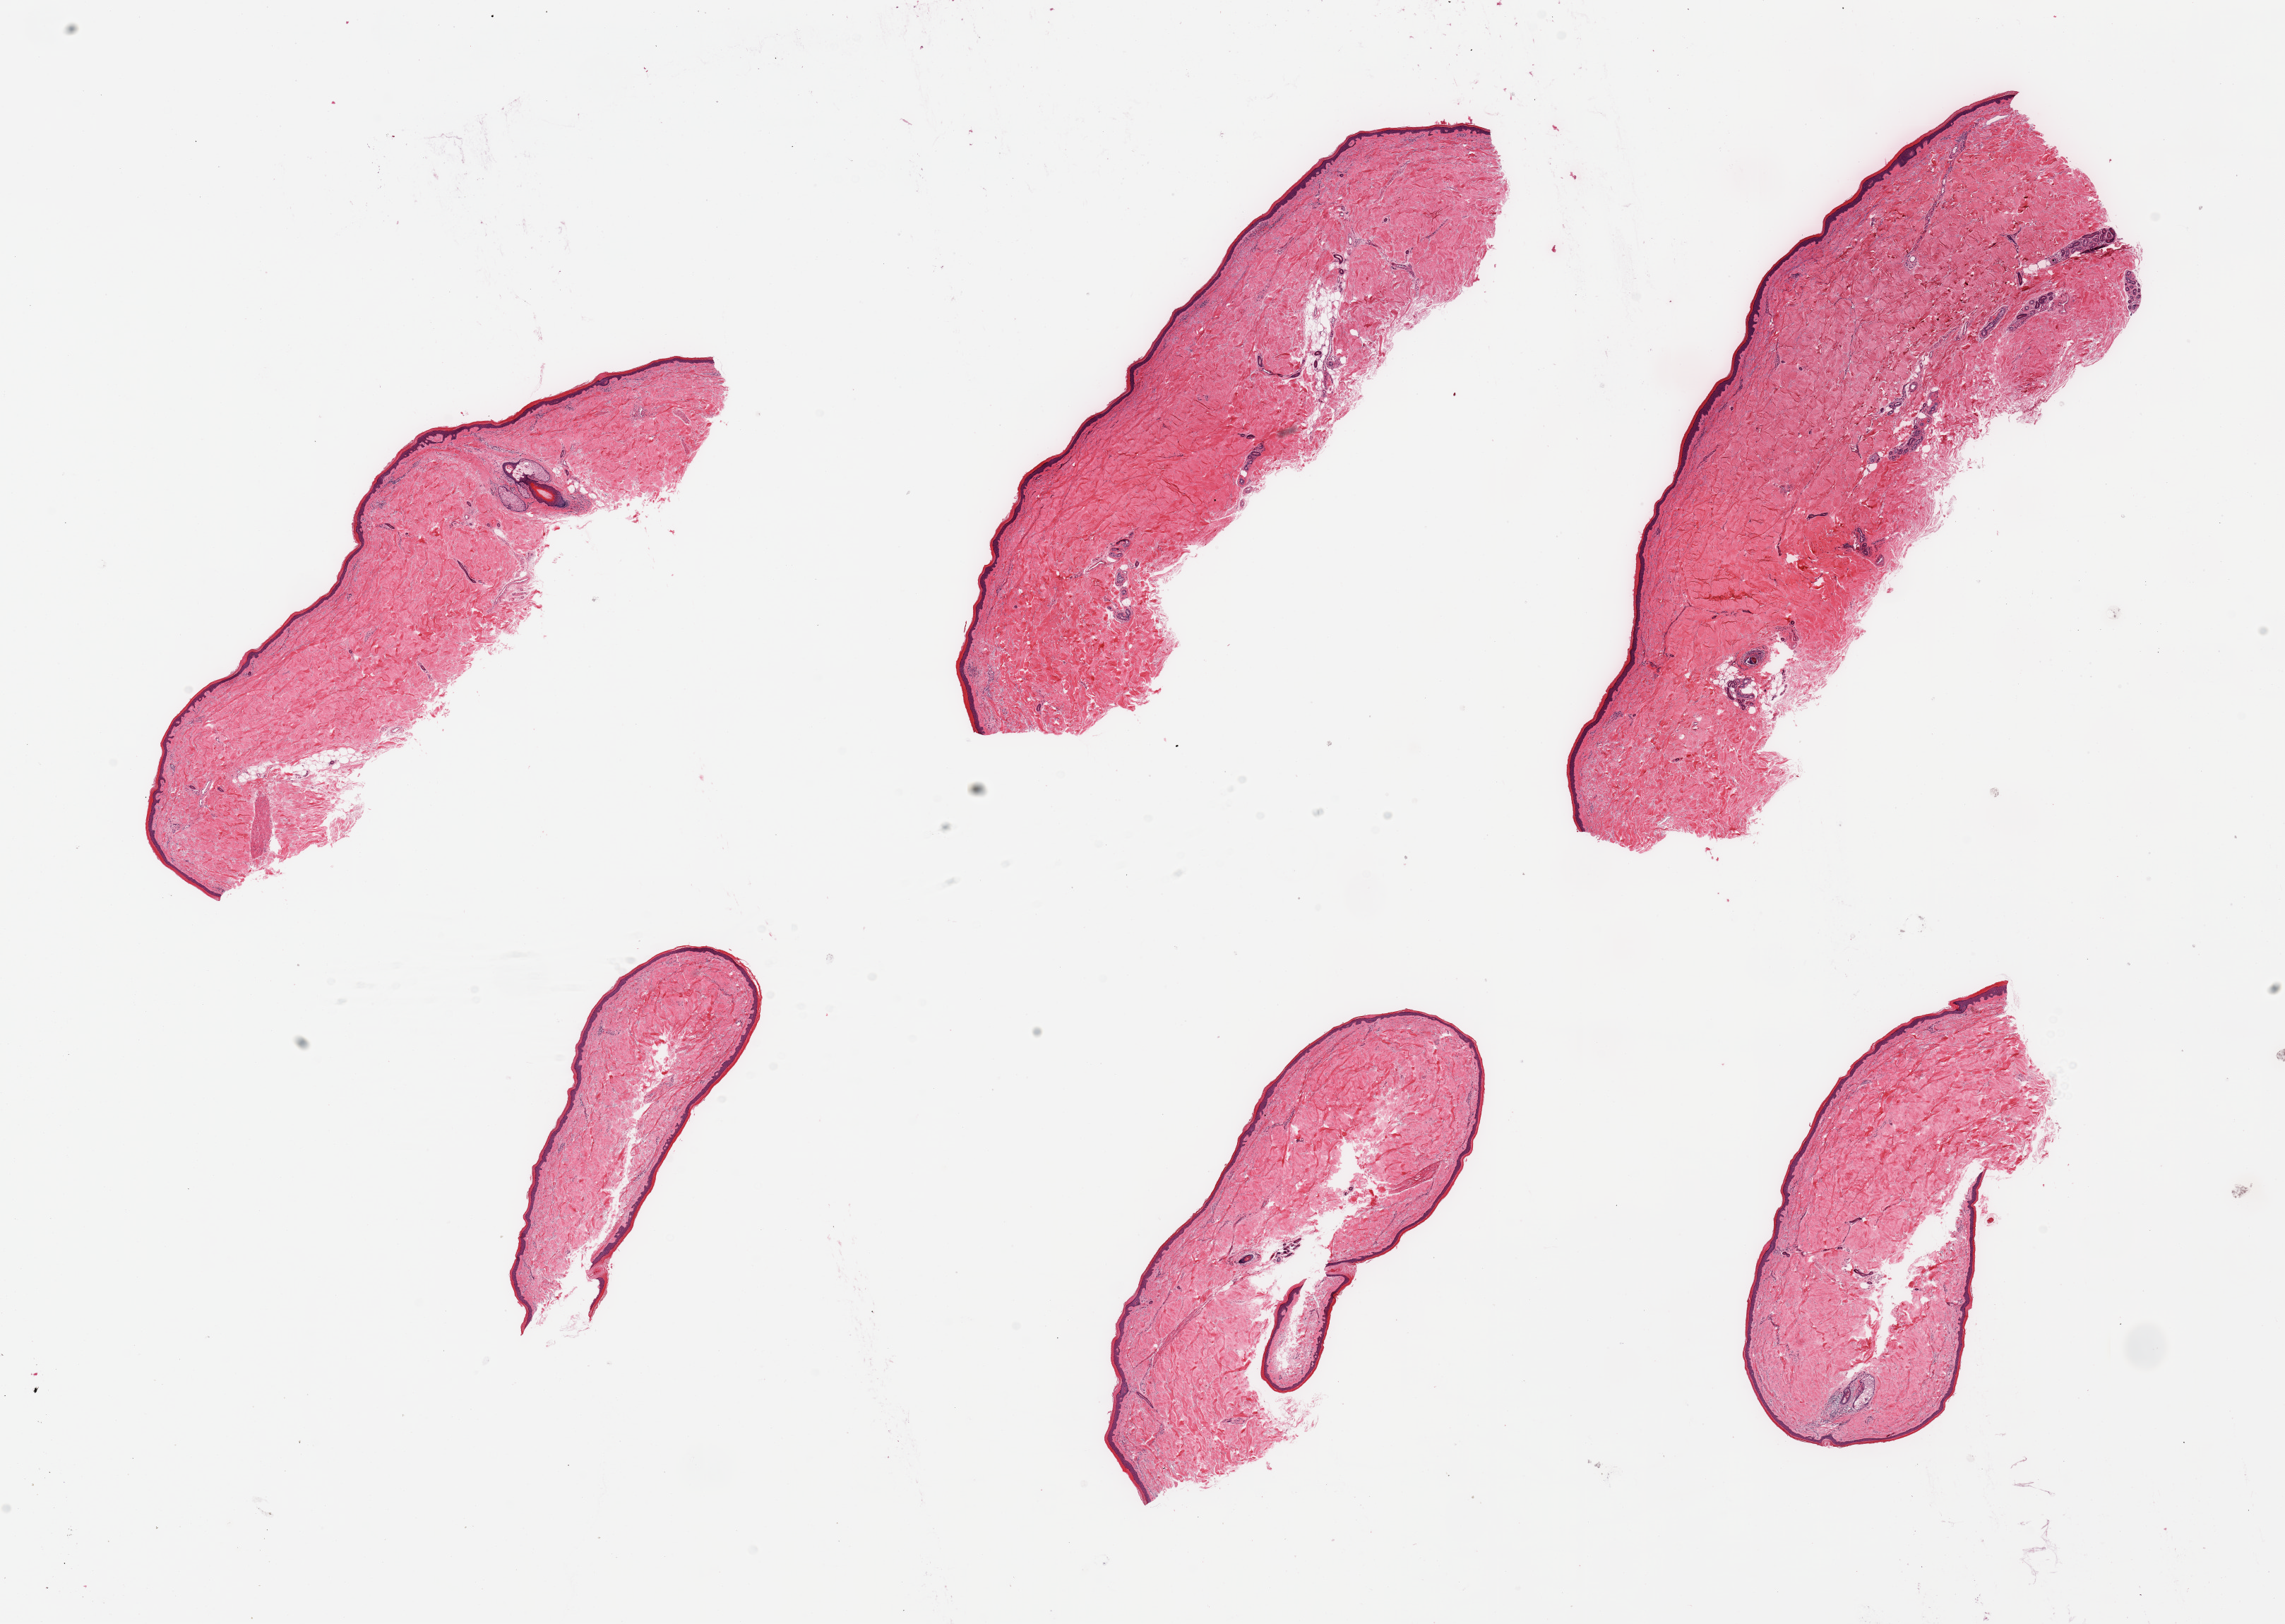
Whole-slide image, H&E stain, a low-resolution overview of the entire scanned area, about 25.6 x 18.2 mm, PAXgene-fixed paraffin-embedded (PFPE) section, sampled site (target tissue): skin of lower leg, tissue donor sample. Donor: male.
- review note (as recorded): 6 pieces; well trimmed, epidermis measures 35 to 48 um thick